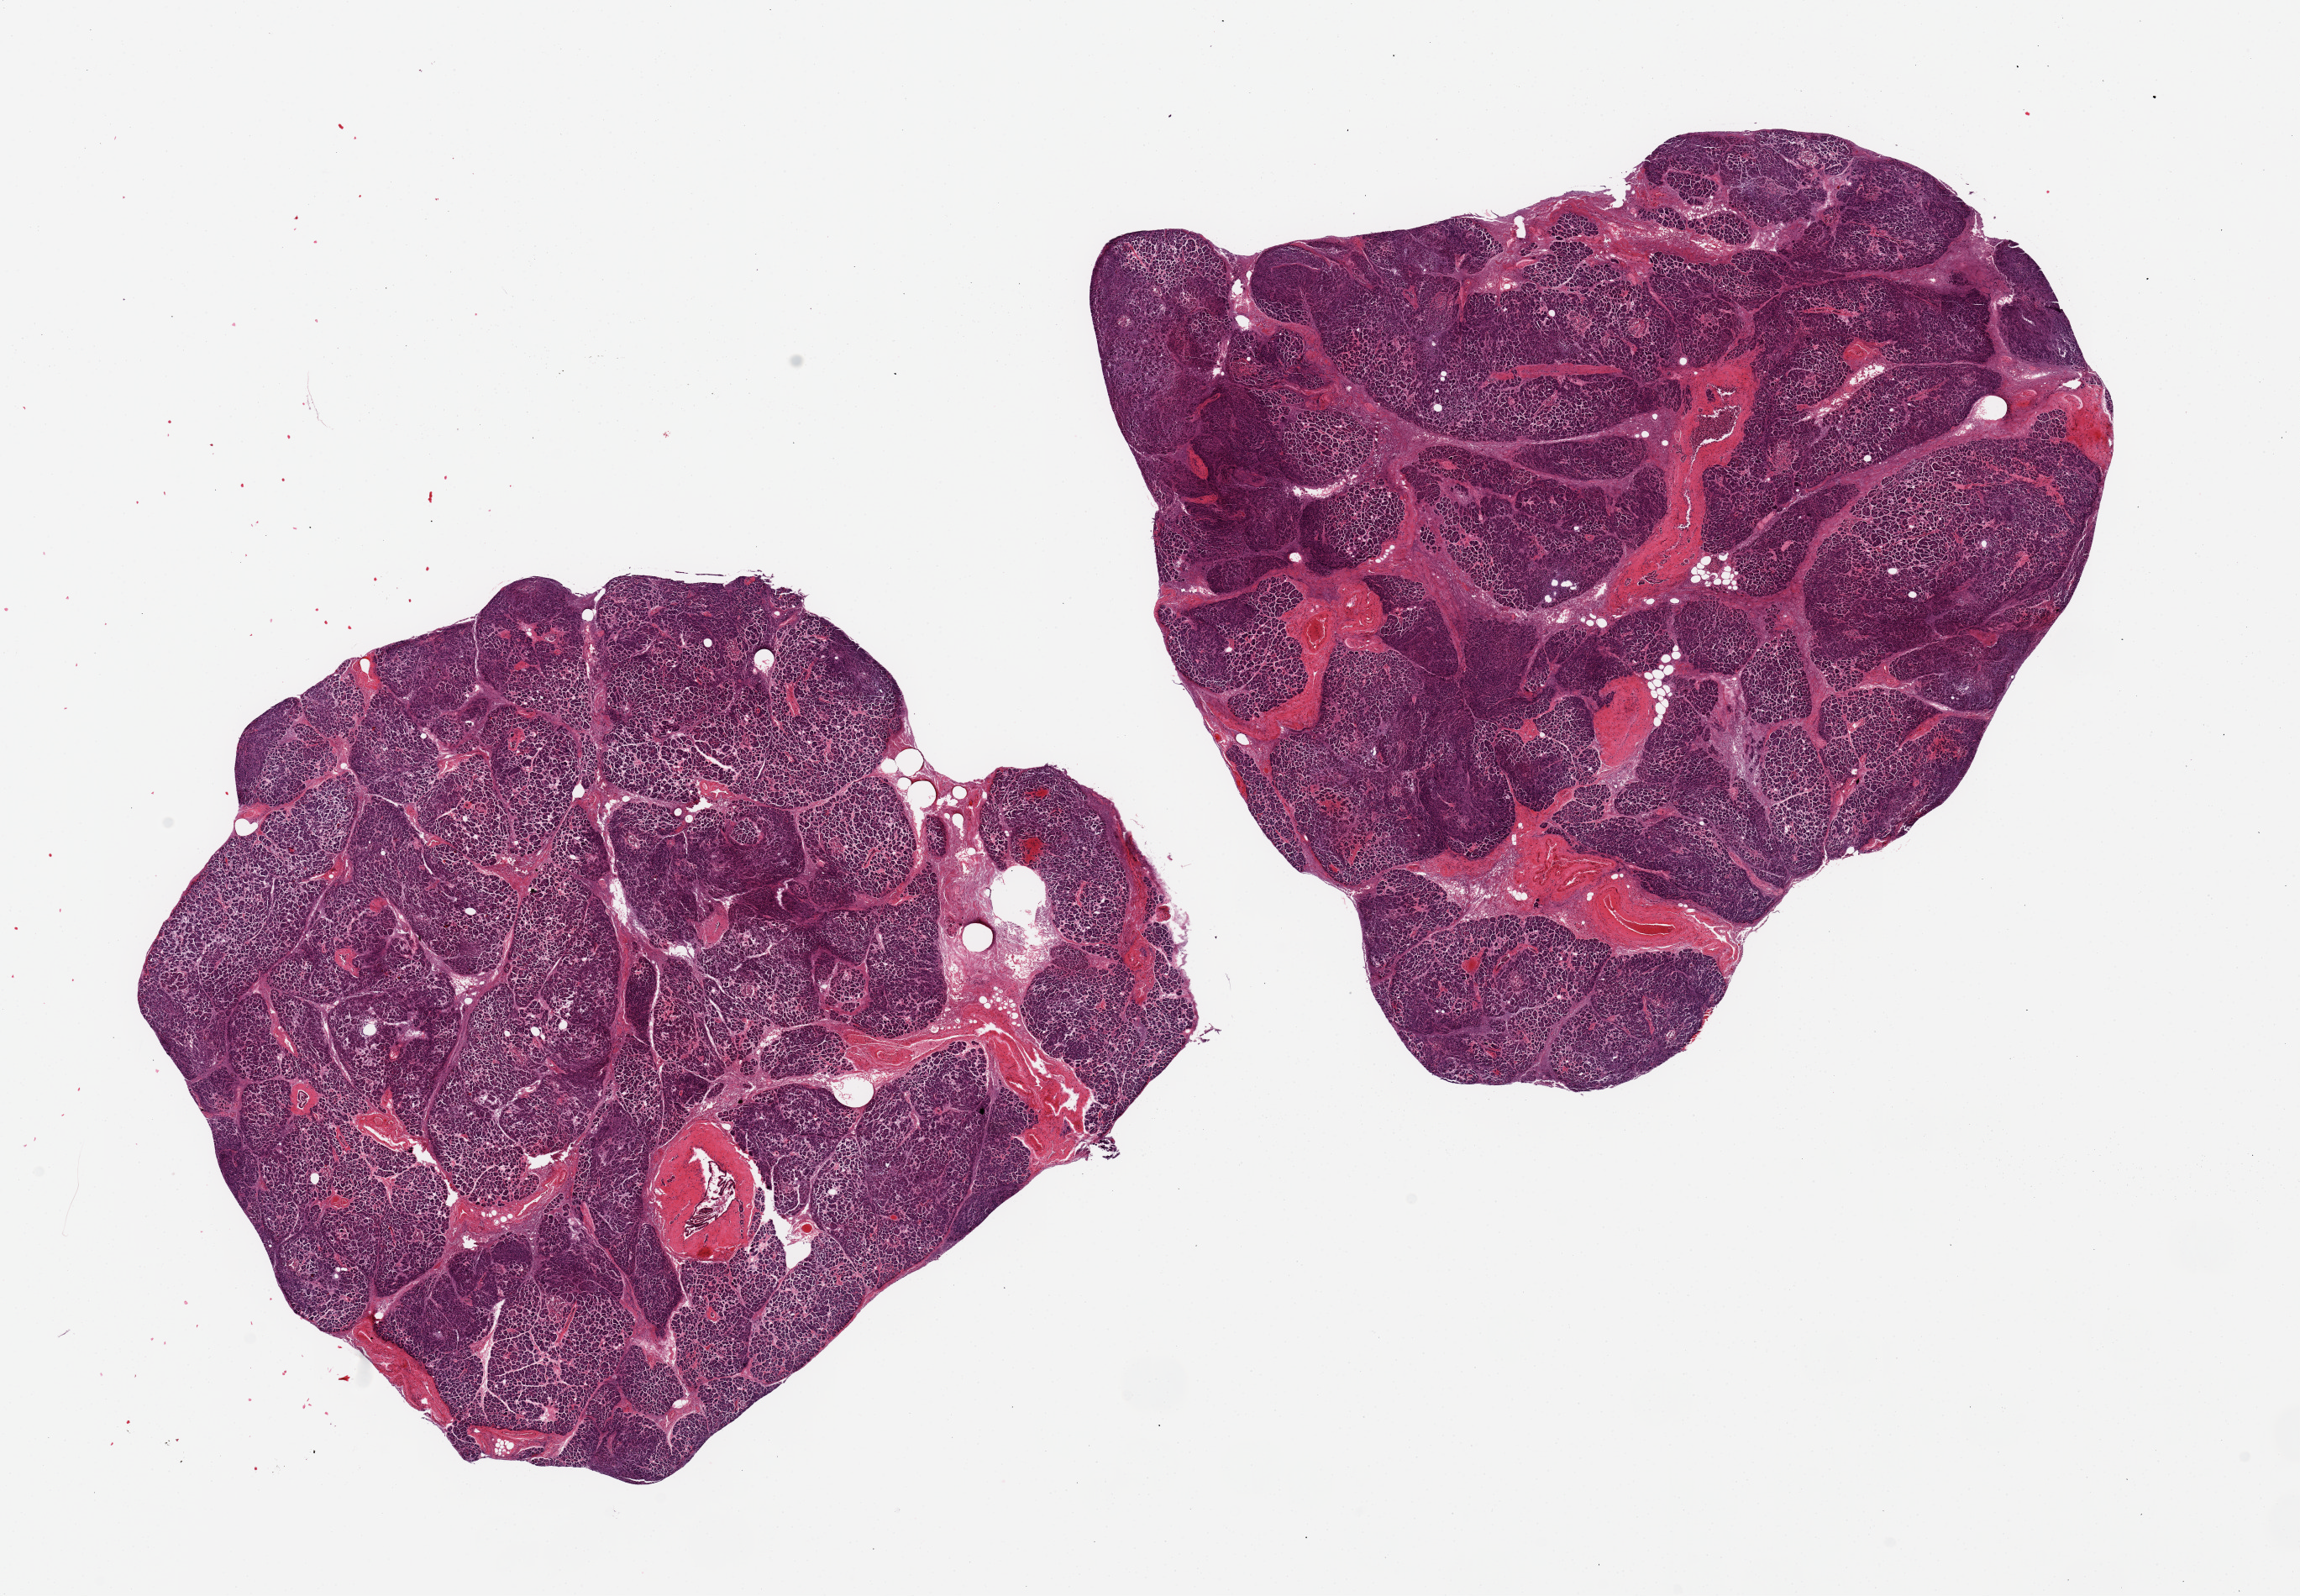
Whole-slide image, haematoxylin and eosin stain, brightfield — shown as a low-resolution overview of the whole scanned area (about 21.7 x 15.0 mm, slide scanned at 20x), PAXgene-fixed, paraffin-embedded tissue, section of pancreas (target tissue), tissue donor sample. Female donor.
Pathologist's review note for this sample: 2 pieces; intraacinar and perilobular fibrosis; Islets noted.